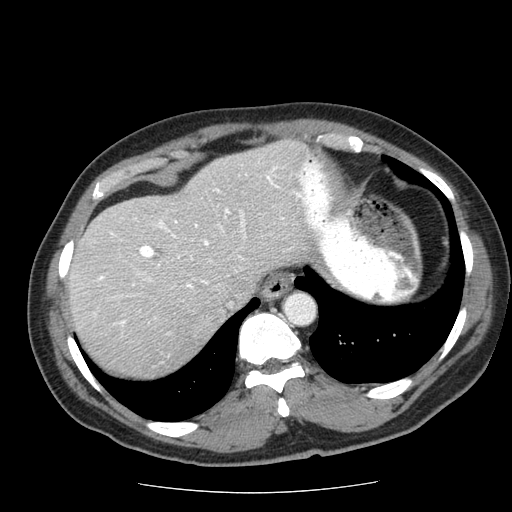
Contrast-enhanced abdominal CT (liver protocol), one axial slice; position 51 of 85 along the scan axis; 120 kVp; soft-tissue window (W 400 / L 40 HU); 2.5 mm slice thickness; 512 × 512 image matrix, field of view 360 × 360 mm. Case-level facts recorded for this patient, not image findings: diagnosis: hepatocellular carcinoma (patient treated with transarterial chemoembolisation; whether this scan precedes or follows treatment is not stated here); TNM stage (as recorded): Stage-IIIA; Child-Pugh class: A; tumour differentiation: well differentiated.
Outlined on this slice (semi-automatically segmented with operator editing):
- liver parenchyma outside the tumour (the mass and vessels are separate outlines, so this box may not span the whole liver): bounding box <68,140,330,376> (left, top, right, bottom; pixels)
- liver vessels: <97,162,329,326>